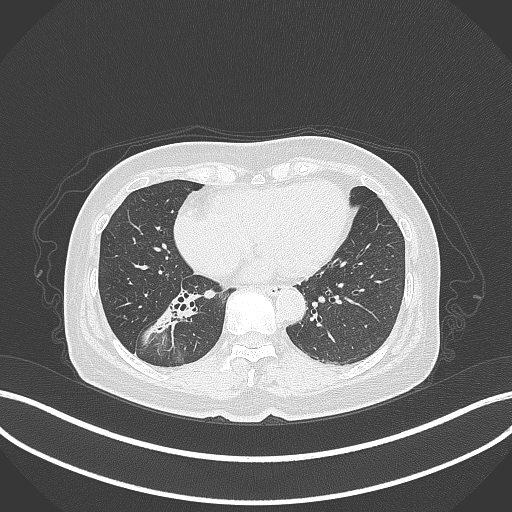
Chest CT, one axial slice. Reconstruction kernel B70f. Lung window (W 1500 / L -600 HU). 512 × 512 image matrix, field of view 400 × 400 mm. Patient: female, 67 years. From the clinical record (not read from this slice): clinical TNM (as recorded): T1c N1 M0.
Outlined on this slice (rectangle marked by the reading radiologist):
- lung tumour (recorded histology: adenocarcinoma): bounding box [x1, y1, x2, y2] px = [139, 291, 203, 350]